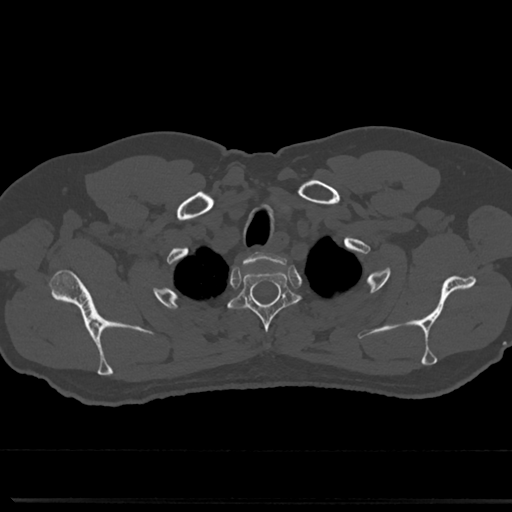
CT including the spine, one axial slice; slice 638 of 817 in the series (ordered by position); reconstruction kernel Br40s/3; bone window (W 1800 / L 400 HU); 0.5 mm slice thickness; 512 × 512 image matrix, field of view 355 × 355 mm. Patient: male, 61 years. Case-level facts recorded for this patient, not image findings: primary cancer: prostate.
Outlined on this slice (semi-automatically segmented with operator editing):
- T2 vertebra: bounding box <232,263,296,354> (left, top, right, bottom; pixels)
- T3 vertebra: <305,315,309,322>